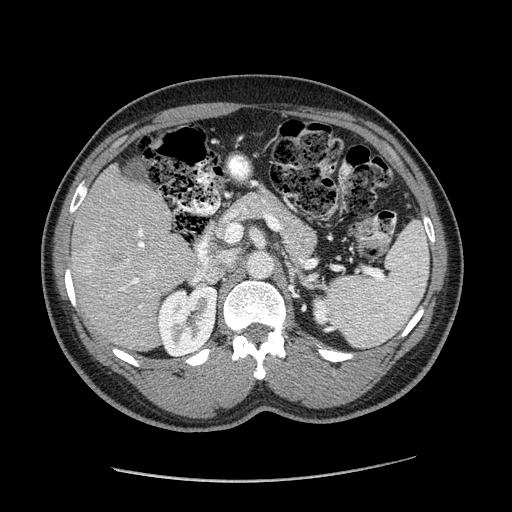
Contrast-enhanced abdominal CT (liver protocol), one axial slice; soft-tissue window (W 400 / L 40 HU); 512 × 512 image matrix, field of view 400 × 400 mm. From the clinical record (not read from this slice): diagnosis: hepatocellular carcinoma (patient treated with transarterial chemoembolisation; whether this scan precedes or follows treatment is not stated here); TNM stage (as recorded): Stage-I; Child-Pugh class: A; tumour differentiation: well differentiated; tumour nodularity: uninodular.
Annotated regions visible in this slice (semi-automatic segmentation, software-assisted and operator-edited):
- liver parenchyma outside the tumour (the mass and vessels are separate outlines, so this box may not span the whole liver): bounding box <70,164,214,350> (left, top, right, bottom; pixels)
- mass: <90,233,132,270>
- liver vessels: <79,229,209,309>